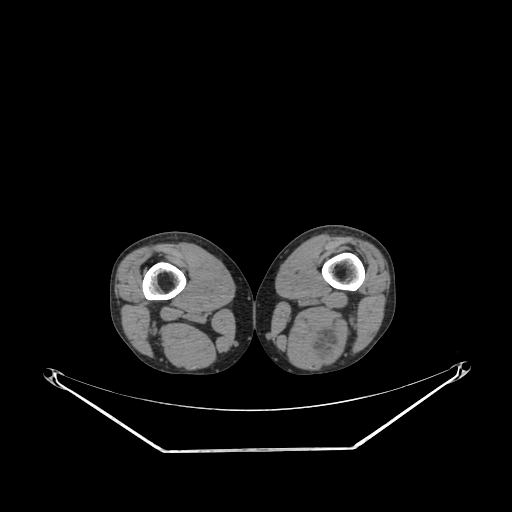
CT of an extremity soft-tissue mass (from a PET/CT study), one axial slice; reconstruction kernel SOFT; soft-tissue window (W 400 / L 40 HU); 512 × 512 image matrix, field of view 500 × 500 mm. Male patient. Case-level facts recorded for this patient, not image findings: histological type: synovial sarcoma; site of the primary tumour: left poplietal fossa.
Outlined on this slice (expert contour drawn on MRI and transferred to this co-registered scan by the dataset authors):
- gross tumour volume (mass): bounding box <308,327,337,362> (left, top, right, bottom; pixels)